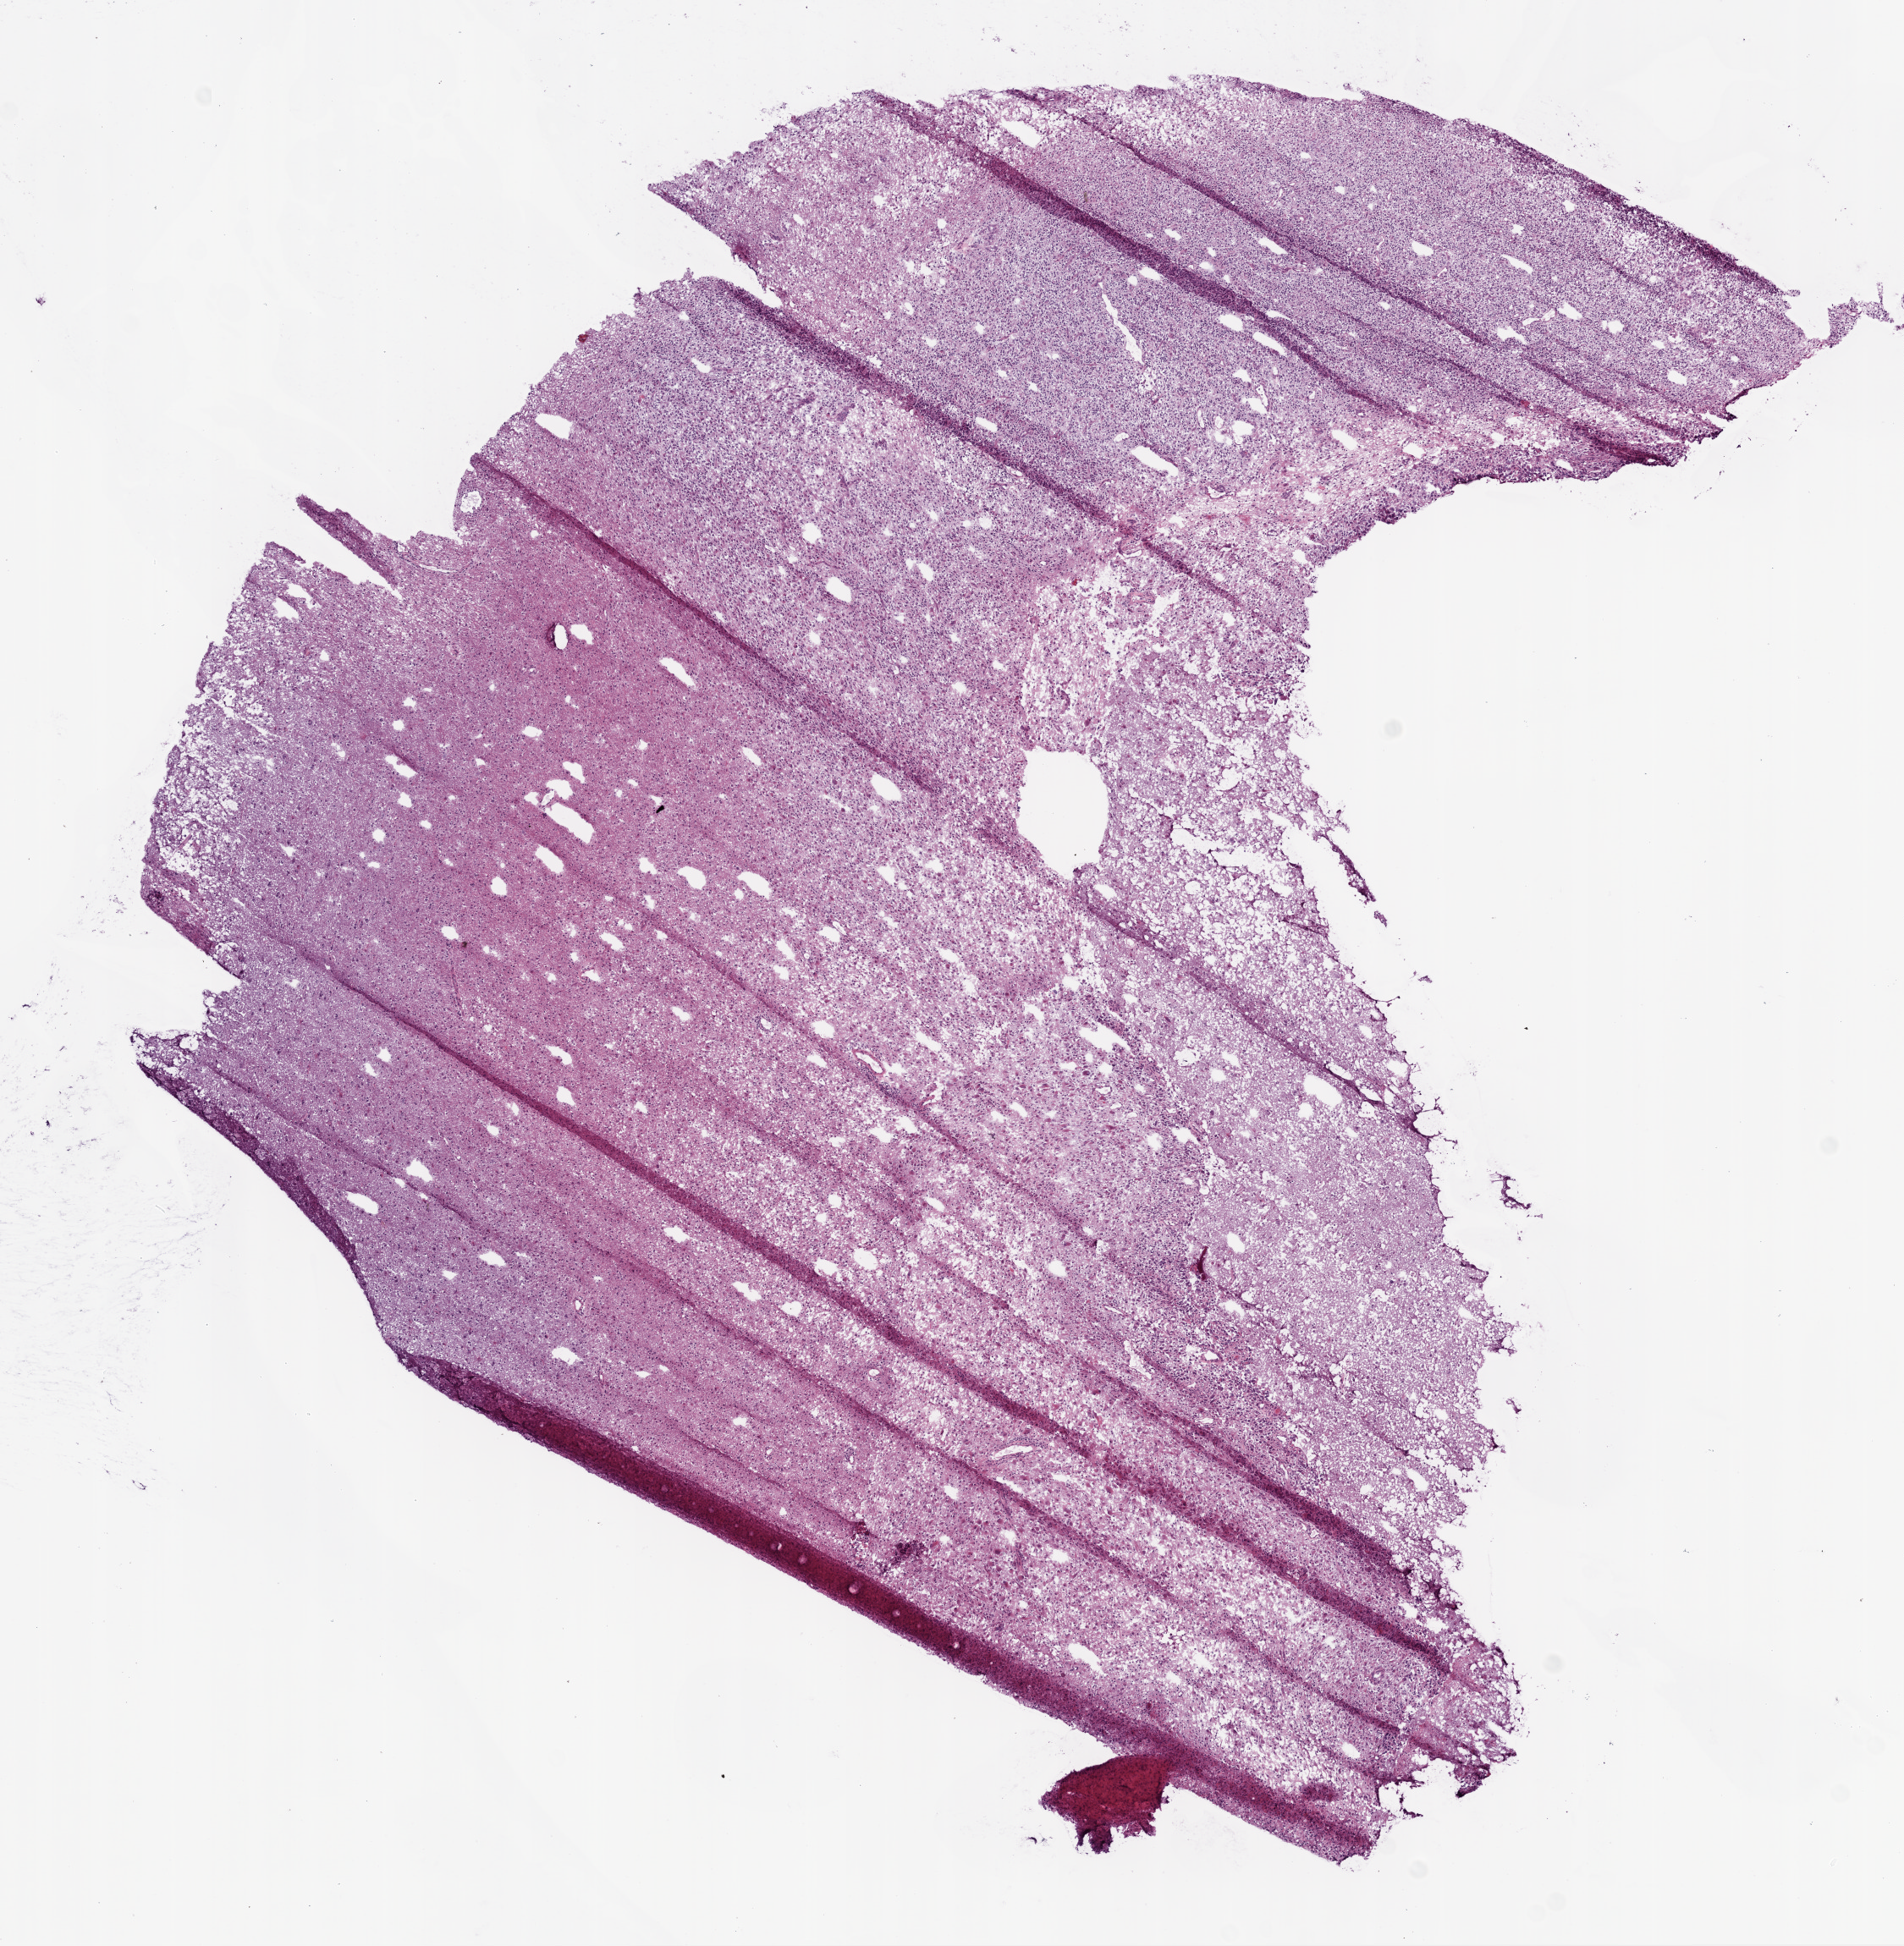
Whole-slide histology image, H&E-stained, whole scanned area (about 9.0 x 9.2 mm) shown as a low-resolution overview. Frozen section from the bottom of the tissue portion. Primary tumour sample from the brain. Female, age 42 years at initial diagnosis. Composition of this section per pathologist review: tumour cells 70%, tumour nuclei 80%, normal cells 25%, stromal cells 5%, necrosis 0%. Infiltration values recorded for this section: lymphocyte infiltration 100%.
Histologic diagnosis: Glioblastoma.